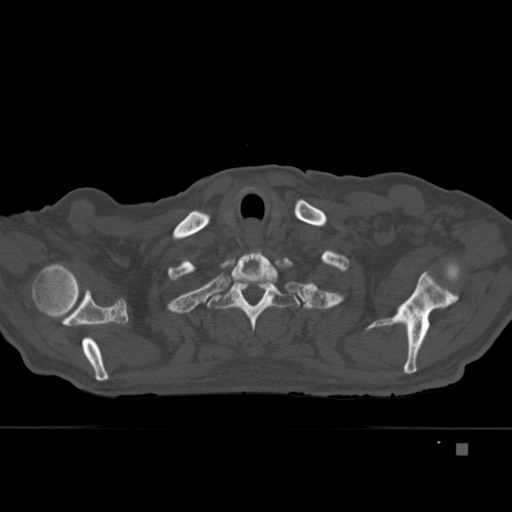
CT including the spine, one axial slice. Slice 351 of 451 in the series (ordered by position). Bone window (W 1800 / L 400 HU). 1.5 mm slice thickness. 512 × 512 image matrix, field of view 378 × 378 mm. Patient: male, 75 years. Case-level facts recorded for this patient, not image findings: primary cancer: prostate.
Annotated regions visible in this slice (semi-automatic segmentation, software-assisted and operator-edited):
- T1 vertebra: bounding box (x1, y1, x2, y2) in pixels: (231, 250, 278, 297)
- T2 vertebra: (203, 276, 300, 332)